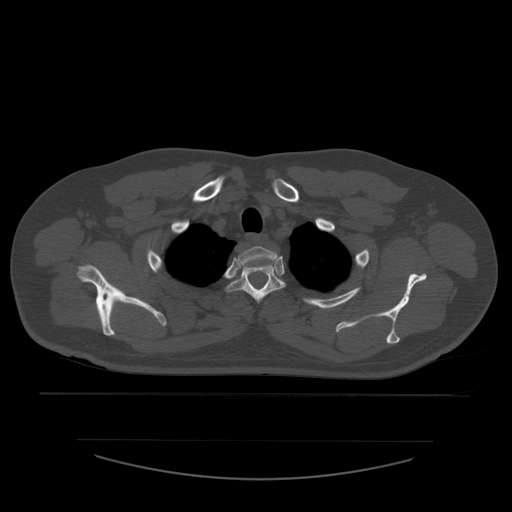
CT including the spine, one axial slice. Position 454 of 532 along the scan axis. 120 kVp. Bone window (W 1800 / L 400 HU). 1.25 mm slice thickness. 512 × 512 image matrix. Patient age 44 years. From the clinical record (not read from this slice): primary cancer: soft tissue sarcoma.
Annotated regions visible in this slice (semi-automatically segmented with operator editing):
- T1 vertebra: bounding box <237,246,278,270> (left, top, right, bottom; pixels)
- T2 vertebra: <227,264,286,303>